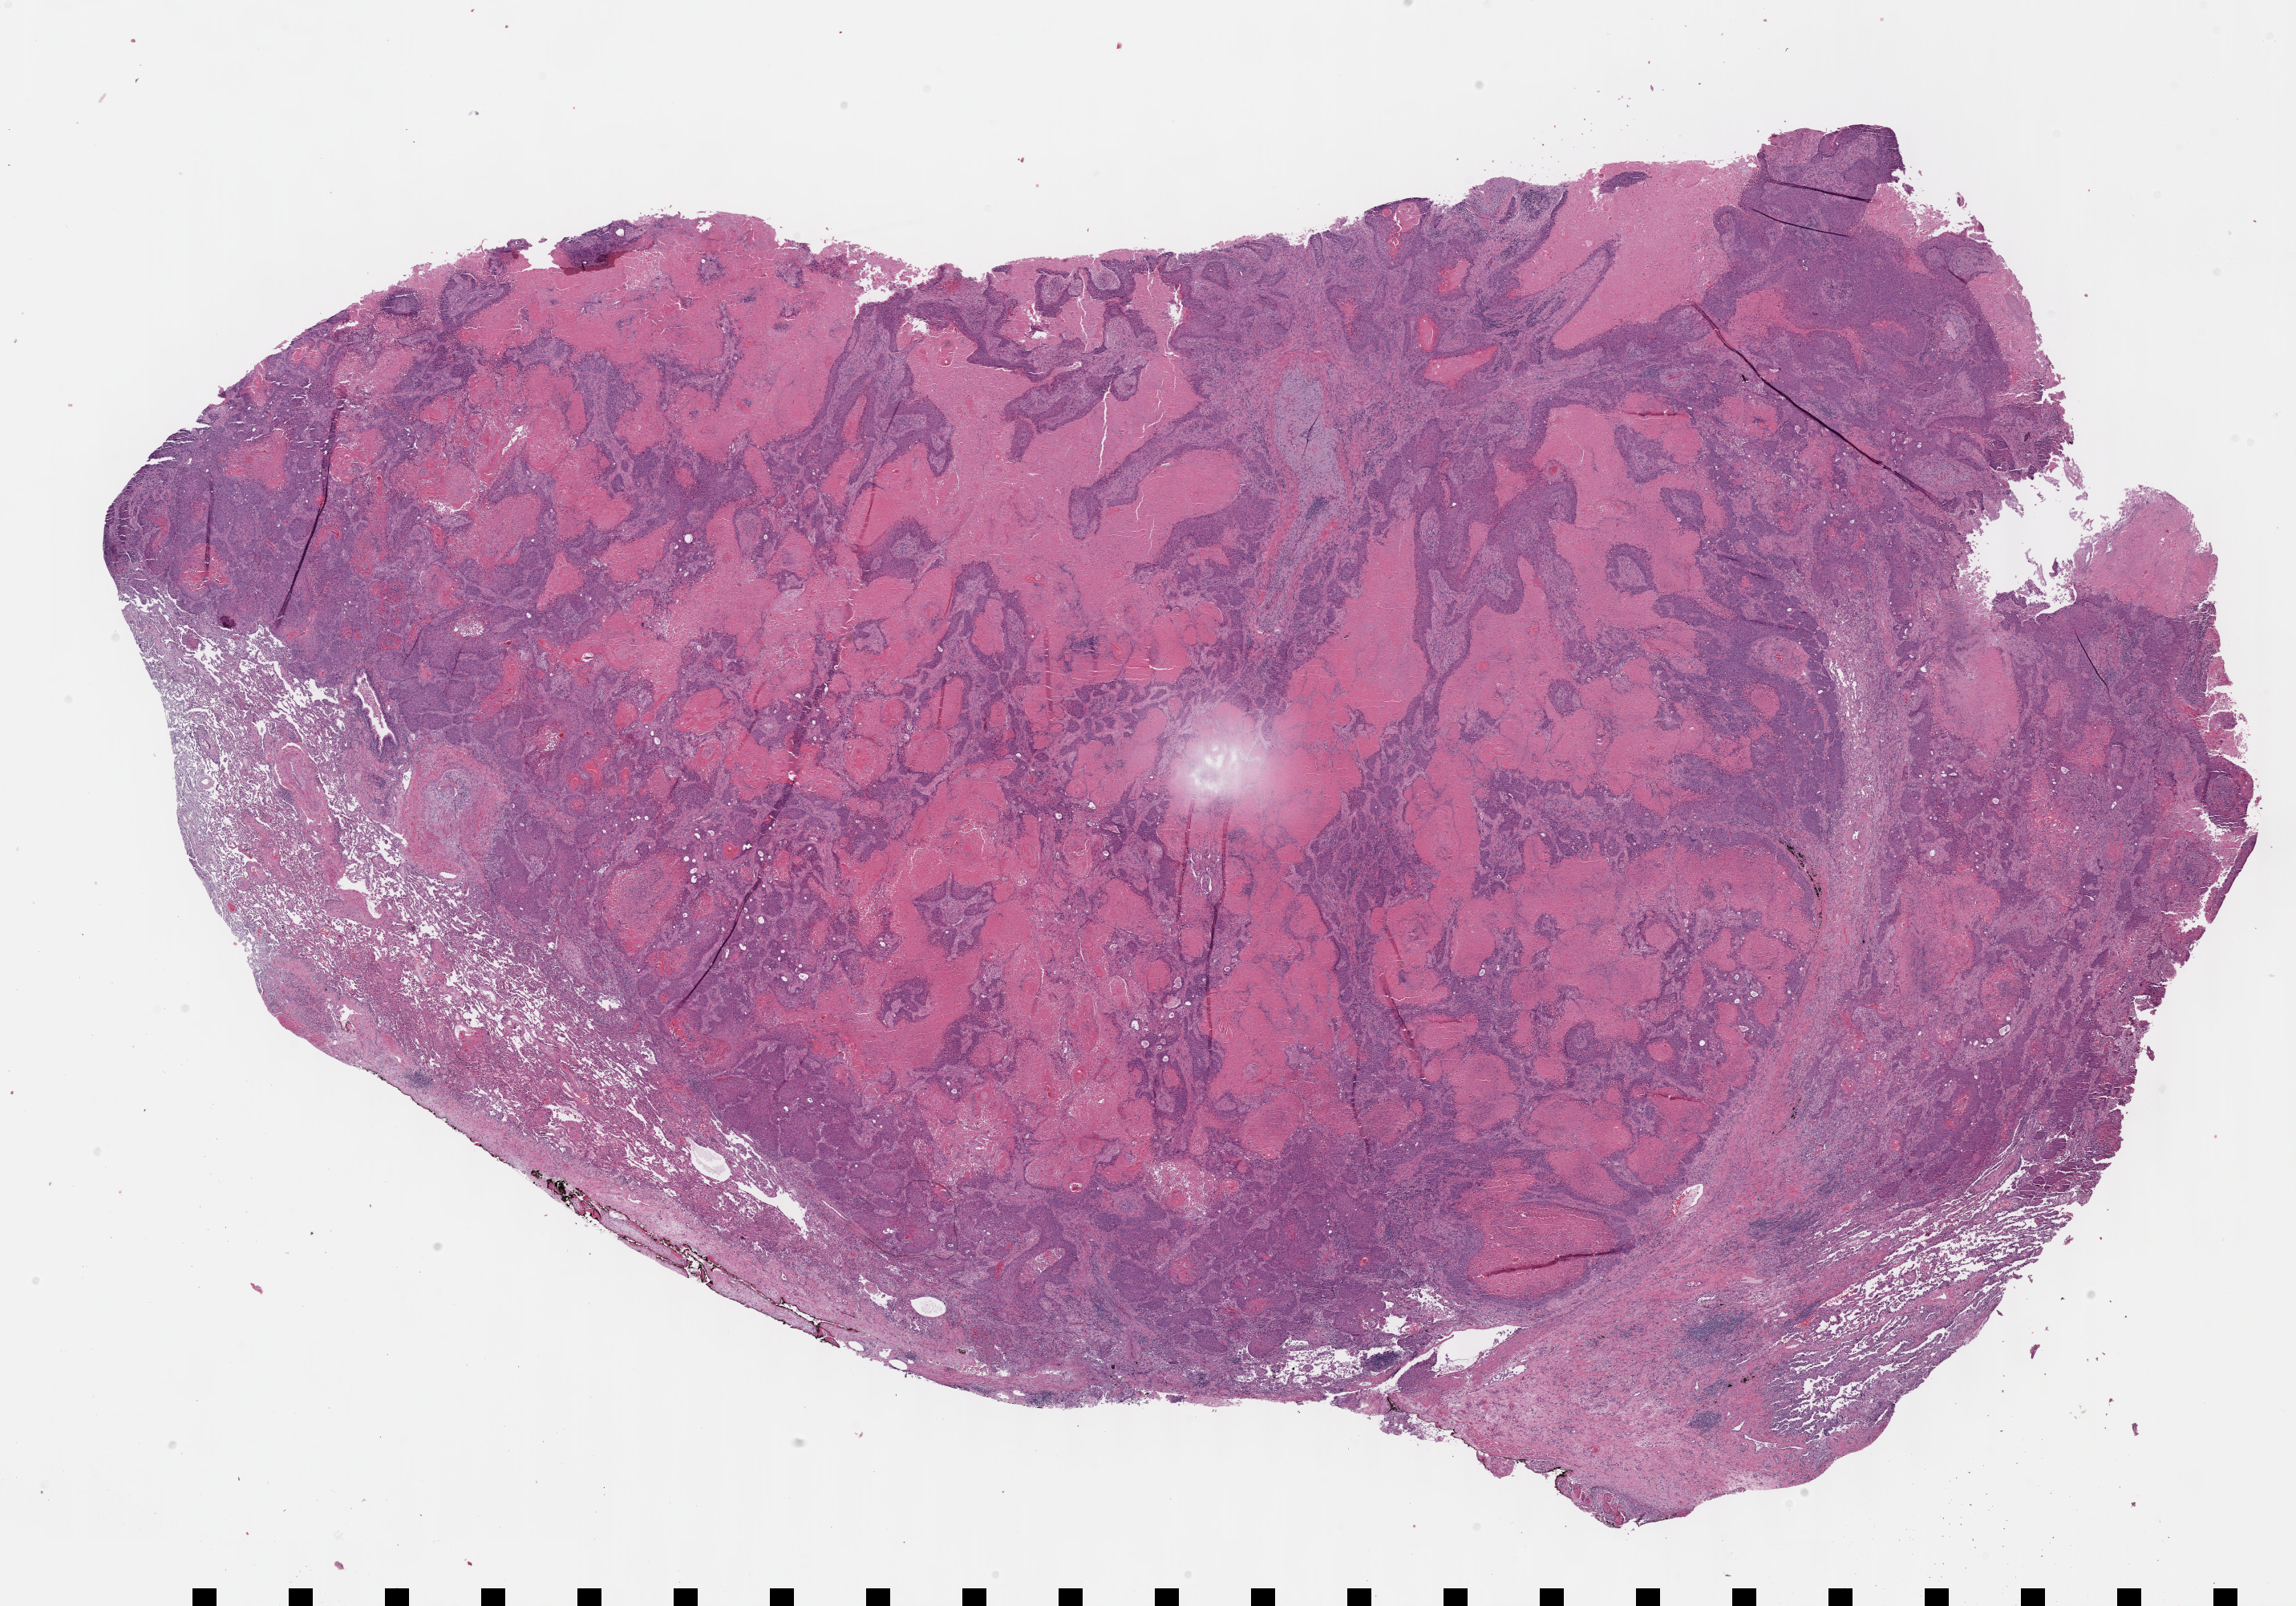
Hematoxylin and eosin (H&E) stained whole-slide image, shown as a low-resolution overview of the whole scanned area (about 23.1 x 16.2 mm); formalin-fixed paraffin-embedded (FFPE) diagnostic section; primary tumour sample from the lung. Male, age 78 years at initial diagnosis.
- diagnosis: Squamous cell carcinoma, NOS